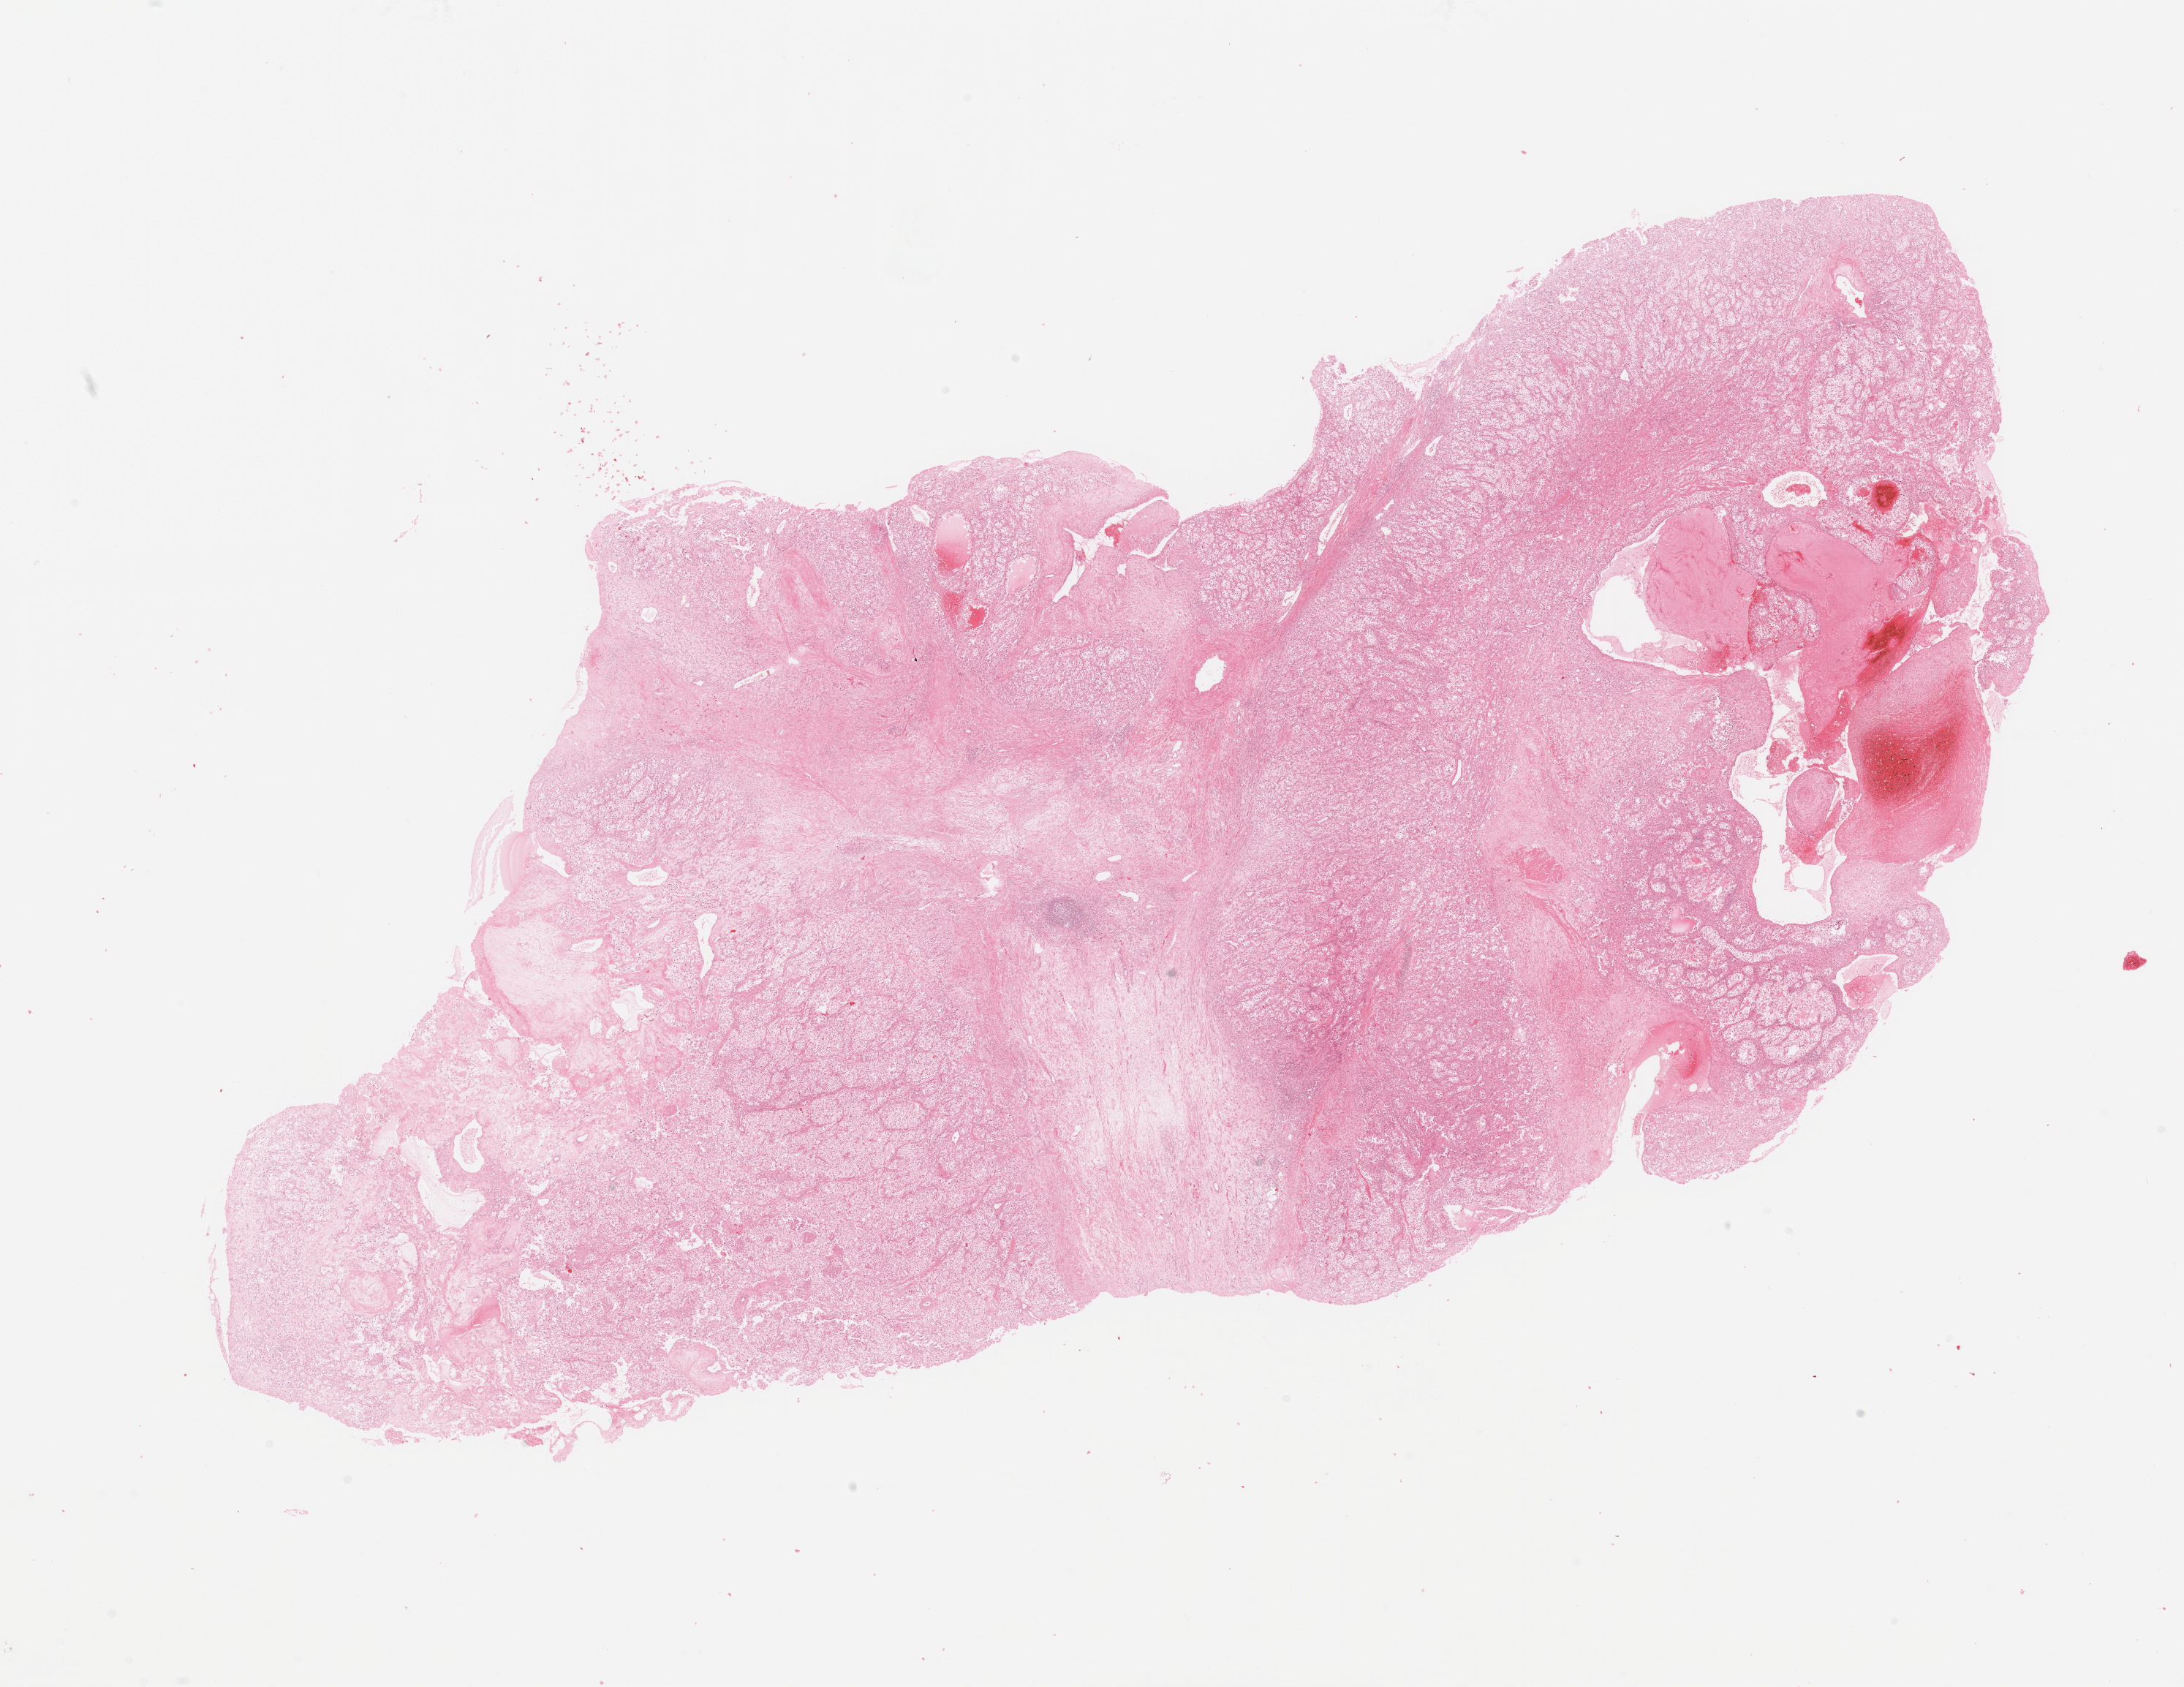
Whole-slide histology image, H&E-stained, whole scanned area (about 23.6 x 18.2 mm) shown as a low-resolution overview. Kidney, tumour tissue. Male, 60 y/o. Histologic grade: G3 (poorly differentiated).
Diagnosis: Renal cell carcinoma, NOS.